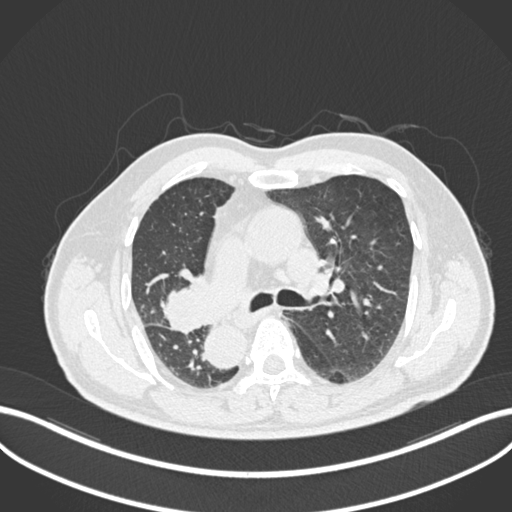
Chest CT, one axial slice. Position 145 of 206 along the scan axis. Reconstruction kernel B30f. Lung window (W 1500 / L -600 HU). 1 mm slice thickness. 512 × 512 image matrix, field of view 400 × 400 mm. Patient: male, 67 years. Case-level facts recorded for this patient, not image findings: clinical TNM (as recorded): T2a N0 M0.
Annotated regions visible in this slice (rectangle marked by the reading radiologist):
- lung tumour (recorded histology: squamous cell carcinoma): box from (x=157, y=269) to (x=211, y=337) px